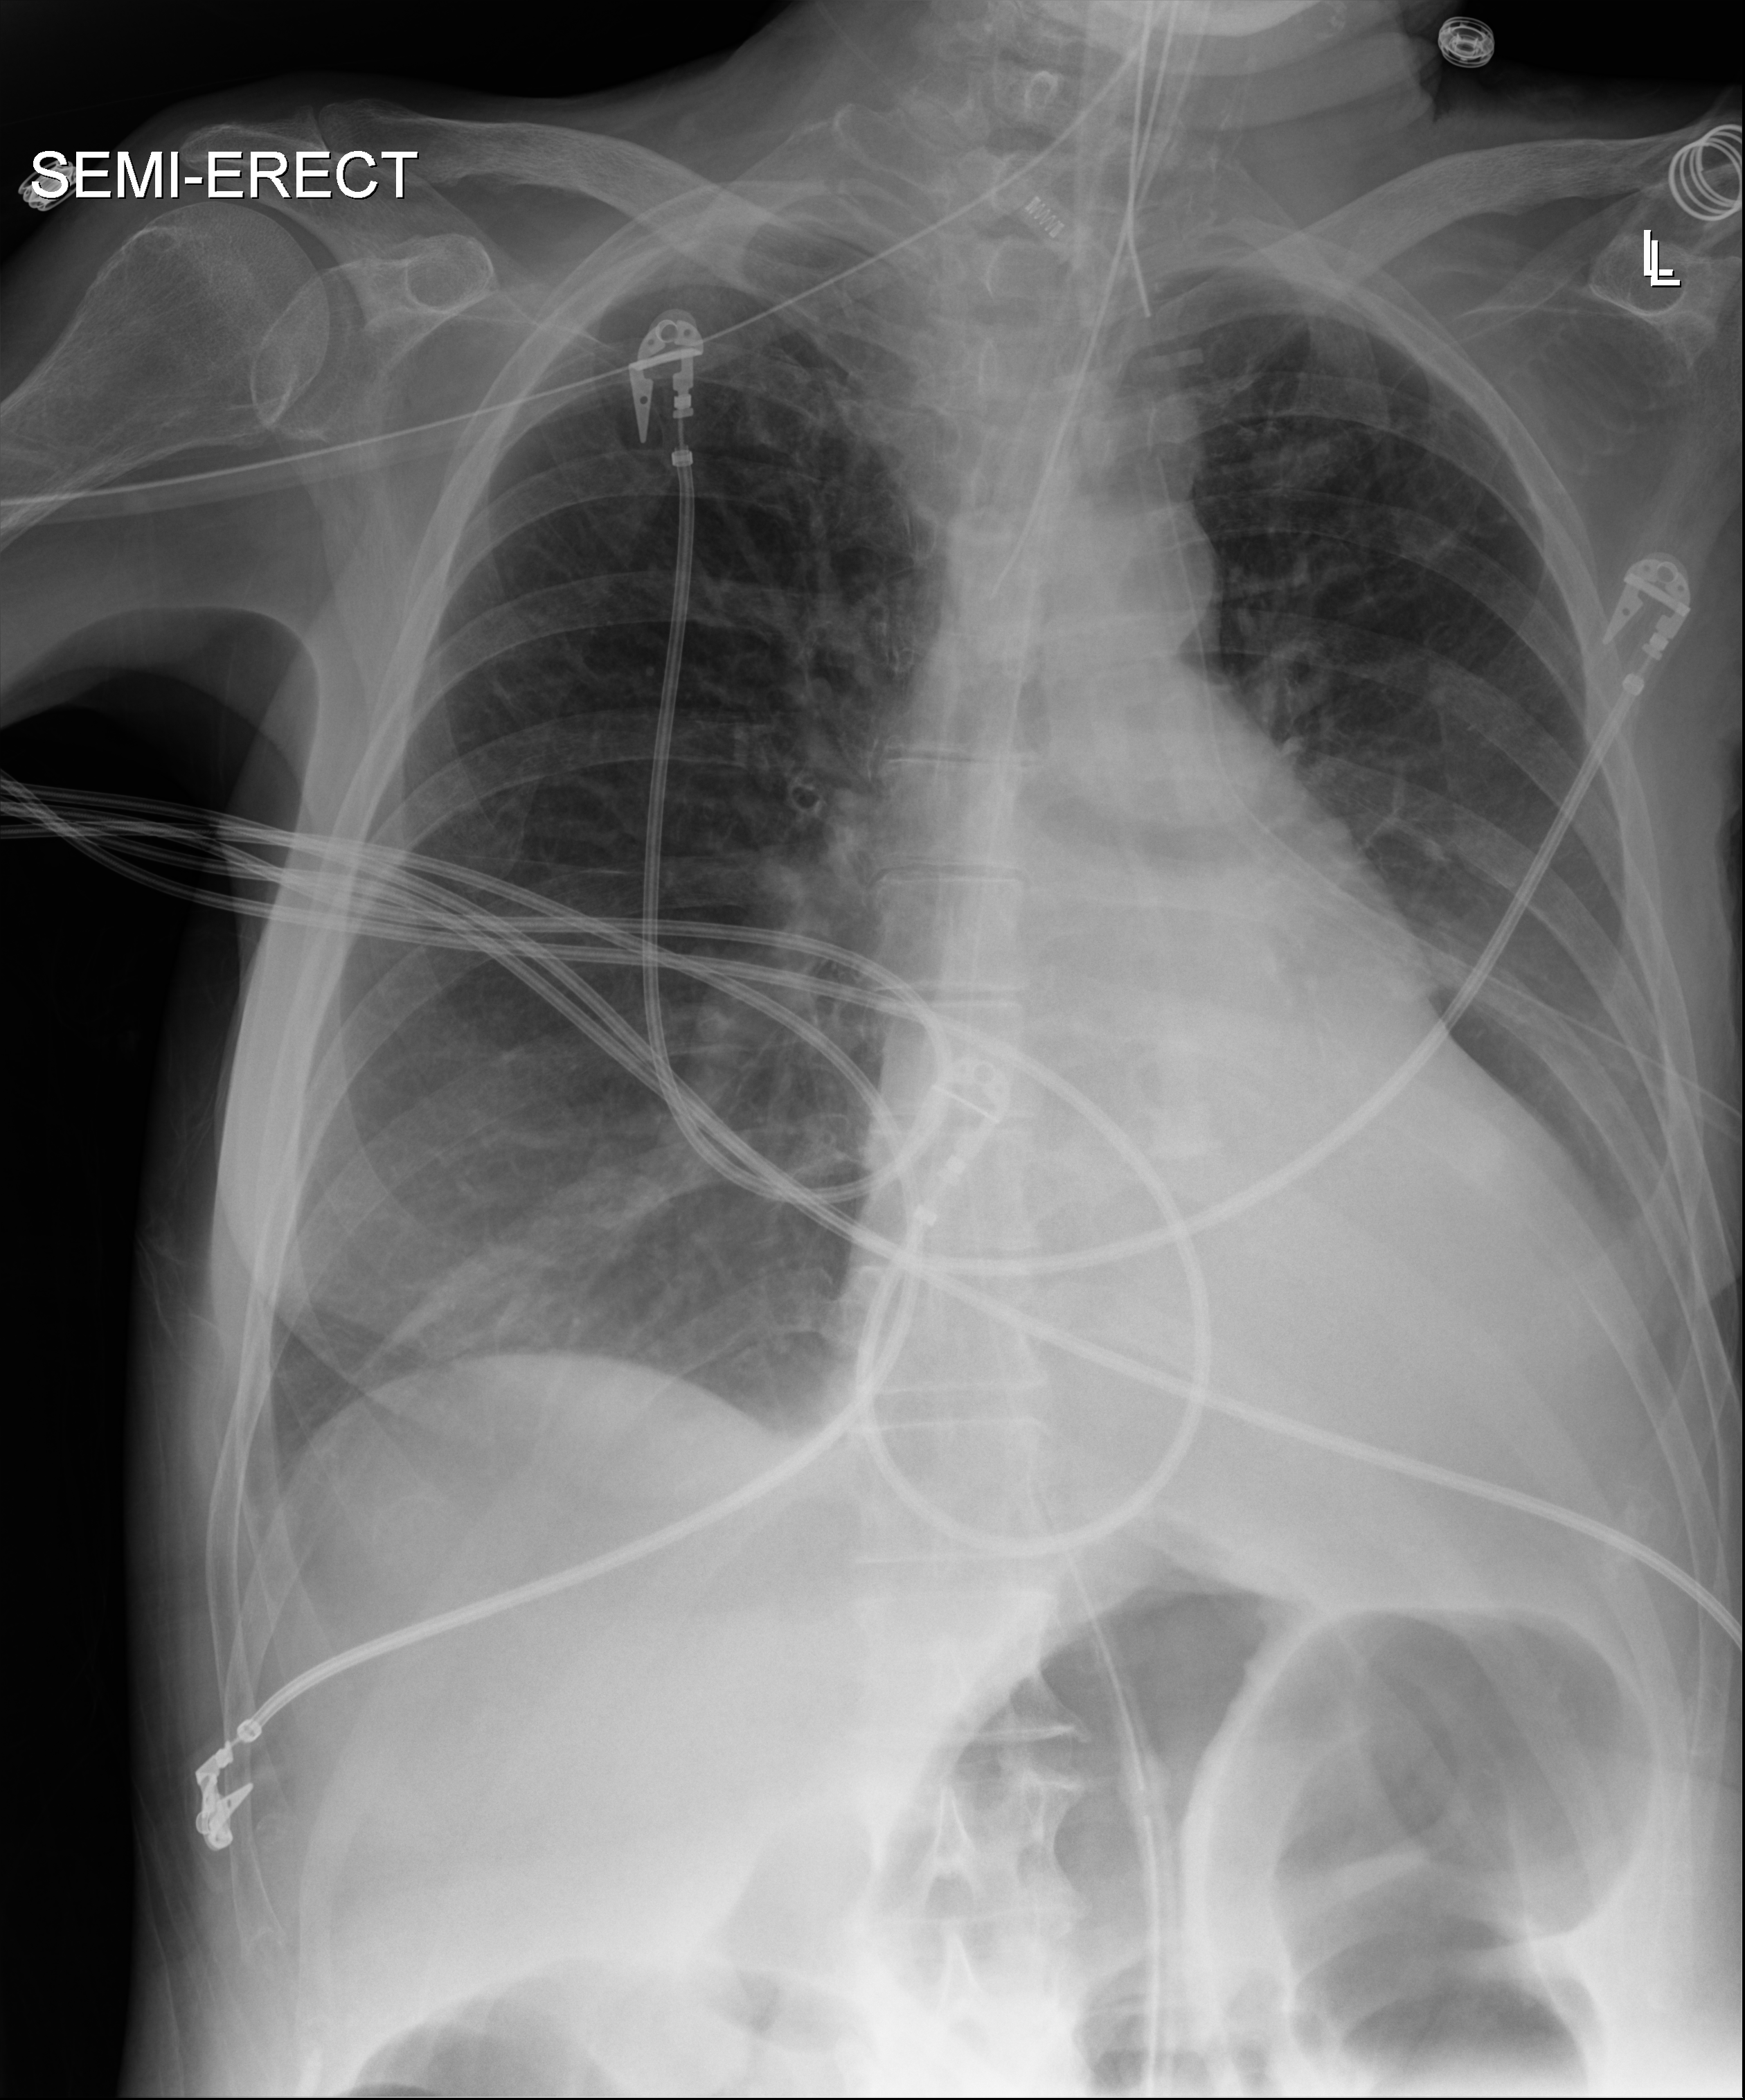
Bedside chest radiograph (digital radiography); anteroposterior (AP) projection. Patient hospitalised with COVID-19; female, aged 60–74 years.
Admission-level facts for this patient (not findings on this image; timing relative to this image not recorded): admitted to intensive care during this hospital stay: yes; mechanically ventilated during this hospital stay: yes.